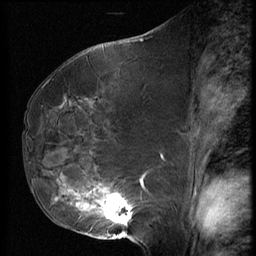
Breast MRI (dynamic contrast-enhanced), one sagittal slice; position 34 of 62 along the scan axis; 3 images stored at this slice position (order not interpretable as contrast timing); 1.5 T; TE 4.2 ms, TR 9 ms; 2.5 mm slice thickness; 256 × 256 image matrix, field of view 180 × 180 mm. Patient: female, 50 years. Case-level facts recorded for this patient, not image findings: setting: breast cancer imaged before/during neoadjuvant chemotherapy; receptor status: HR-positive, HER2-negative.
Outlined on this slice (semi-automatic segmentation, software-assisted and operator-edited):
- analysis volume of interest (the breast-tissue region the enhancement analysis was run in; not a lesion): box from (x=59, y=125) to (x=139, y=238) px
- tumour enhancement mask (voxels above the 140 % enhancement threshold inside the analysis volume of interest): (x=59, y=194)–(x=134, y=222)